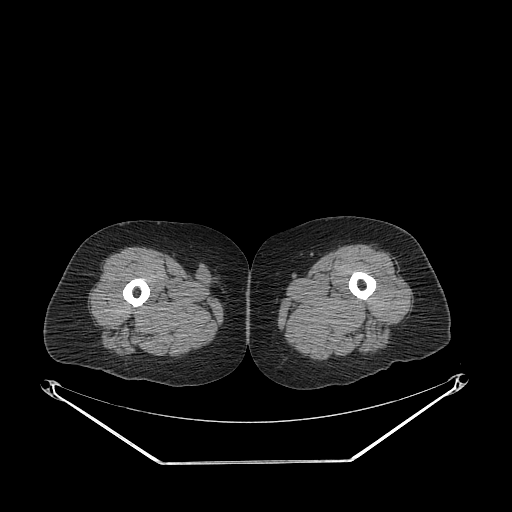
CT of an extremity soft-tissue mass (from a PET/CT study), one axial slice. Position 245 of 311 along the scan axis. Reconstruction kernel STANDARD. 140 kVp. Soft-tissue window (W 400 / L 40 HU). 3.75 mm slice thickness. 512 × 512 image matrix. Female patient. From the clinical record (not read from this slice): histological type: leiomyosarcoma; grade: intermediate; site of the primary tumour: parascapusular.
Annotated regions visible in this slice (expert contour drawn on MRI and transferred to this co-registered scan by the dataset authors):
- gross tumour volume including surrounding oedema: box from (x=196, y=264) to (x=220, y=284) px
- gross tumour volume (mass): (x=198, y=265)–(x=213, y=280)